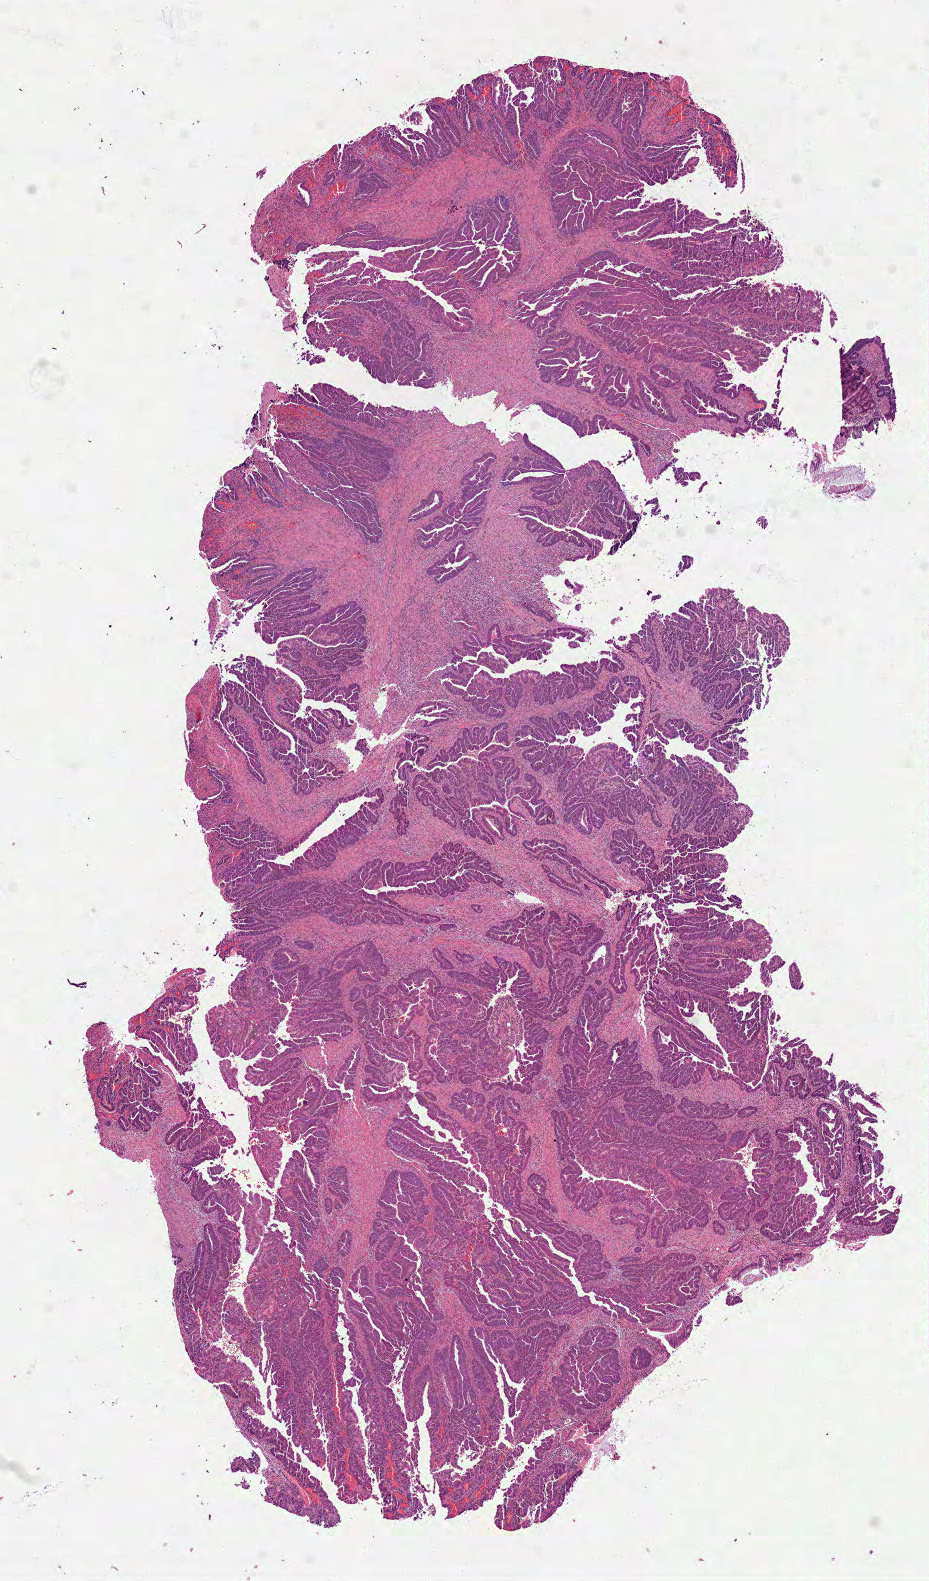
H&E-stained whole-slide image — whole scanned area (about 7.5 x 12.8 mm, from a 40x scan) shown as a low-resolution overview. Formalin-fixed paraffin-embedded (FFPE) diagnostic section. Rectum, primary tumour sample. Male, age 48 years at initial diagnosis.
* AJCC pathologic stage: I
* TNM: T2 N0 M0
* diagnosis: Adenocarcinoma, NOS
* lymph nodes positive (case pathology): 0 of 14 examined